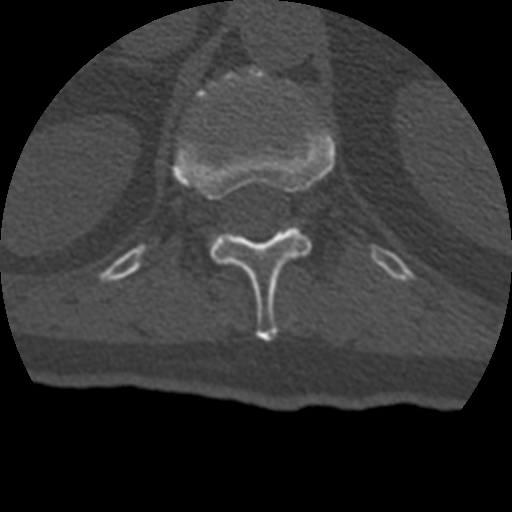
CT including the spine, one axial slice; position 165 of 399 along the scan axis; reconstruction kernel STANDARD; 120 kVp; bone window (W 1800 / L 400 HU); 1.25 mm slice thickness; 512 × 512 image matrix. Patient age 69 years. From the clinical record (not read from this slice): primary cancer: prostate.
Structures marked on this image (semi-automatic segmentation, software-assisted and operator-edited):
- L1 vertebra: bounding box [x1, y1, x2, y2] px = [196, 66, 266, 244]
- T12 vertebra: [173, 126, 335, 341]